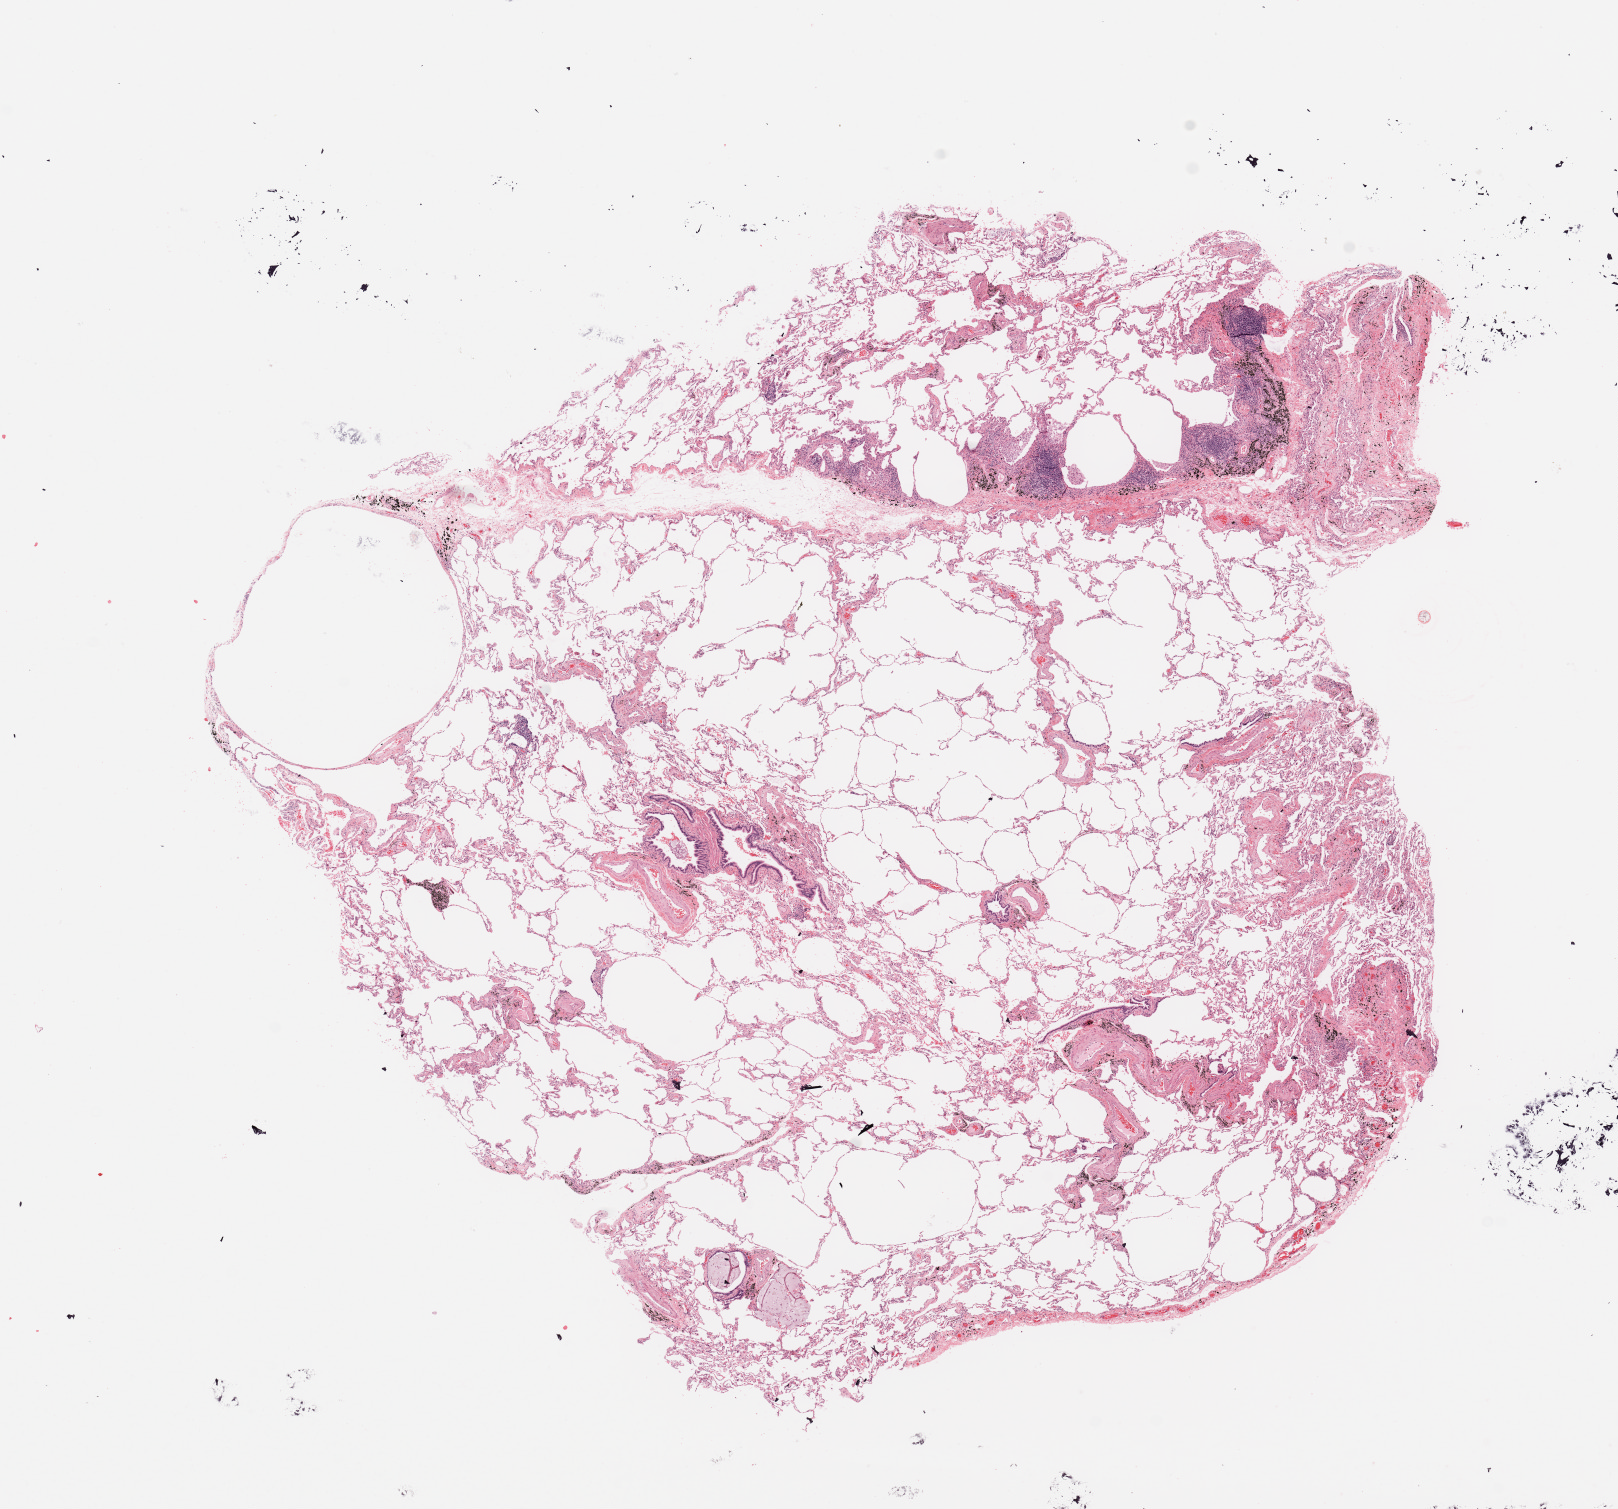
Digitized H&E-stained tissue section (whole slide) — a low-resolution overview of the entire scanned area, about 12.8 x 11.9 mm (acquisition: 20x scan). Normal (non-tumour) tissue sample, sampled site: lung. Patient: female, age 79 years.
This section: normal (non-tumour) tissue from the same patient. Patient diagnosis: Adenocarcinoma, NOS.